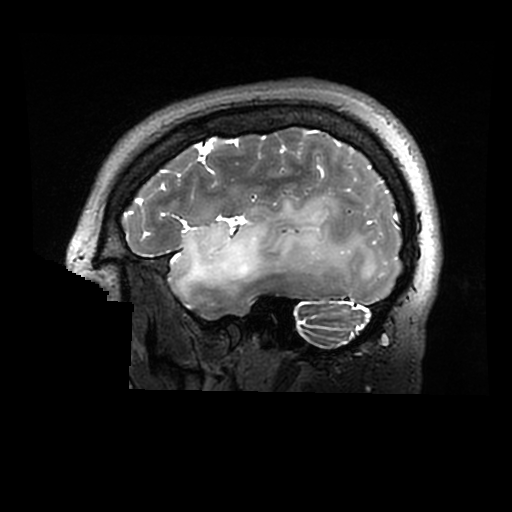
Brain MRI from a brain-tumour surgery series, one sagittal slice. Slice 230 of 320 in the series (ordered by position). 512 × 512 image matrix. From the clinical record (not read from this slice): histopathology: Astrocytoma; WHO grade: 2; IDH mutation: yes.
Structures marked on this image (expert manual segmentation):
- tumour: bounding box <170,195,379,295> (left, top, right, bottom; pixels)